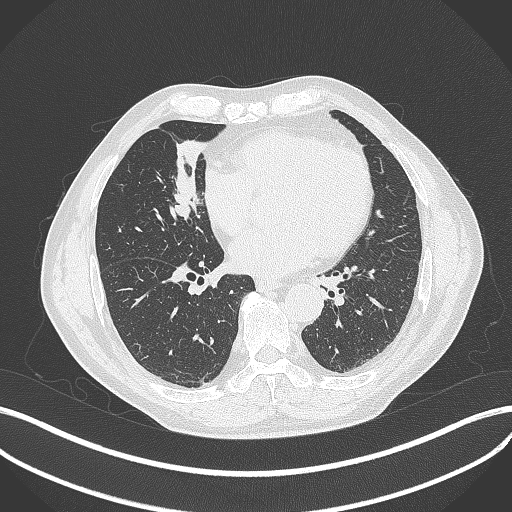
Chest CT, one axial slice; slice 164 of 429 in the series (ordered by position); 120 kVp; lung window (W 1500 / L -600 HU); 1 mm slice thickness; 512 × 512 image matrix. Male patient, age 61 years. Case-level facts recorded for this patient, not image findings: clinical TNM (as recorded): T2b N1 M0.
Structures marked on this image (rectangle marked by the reading radiologist):
- lung tumour (recorded histology: squamous cell carcinoma): bounding box <166,164,209,225> (left, top, right, bottom; pixels)